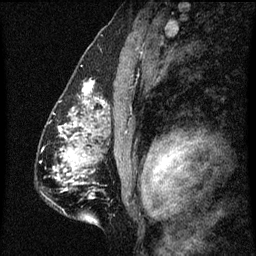
Breast MRI (dynamic contrast-enhanced), one sagittal slice. Position 38 of 60 along the scan axis. Dynamic contrast-enhanced series, image 2 of 3 at this slice position (ordered by acquisition). 1.5 T. TE 4.2 ms, TR 8 ms. 256 × 256 image matrix, field of view 180 × 180 mm. Female patient, age 51 years.
Outlined on this slice (semi-automatically segmented with operator editing):
- analysis volume of interest (the breast-tissue region the enhancement analysis was run in; not a lesion): bounding box [x1, y1, x2, y2] px = [61, 82, 102, 129]
- tumour enhancement mask (voxels above the 70 % enhancement threshold inside the analysis volume of interest): [72, 82, 102, 129]